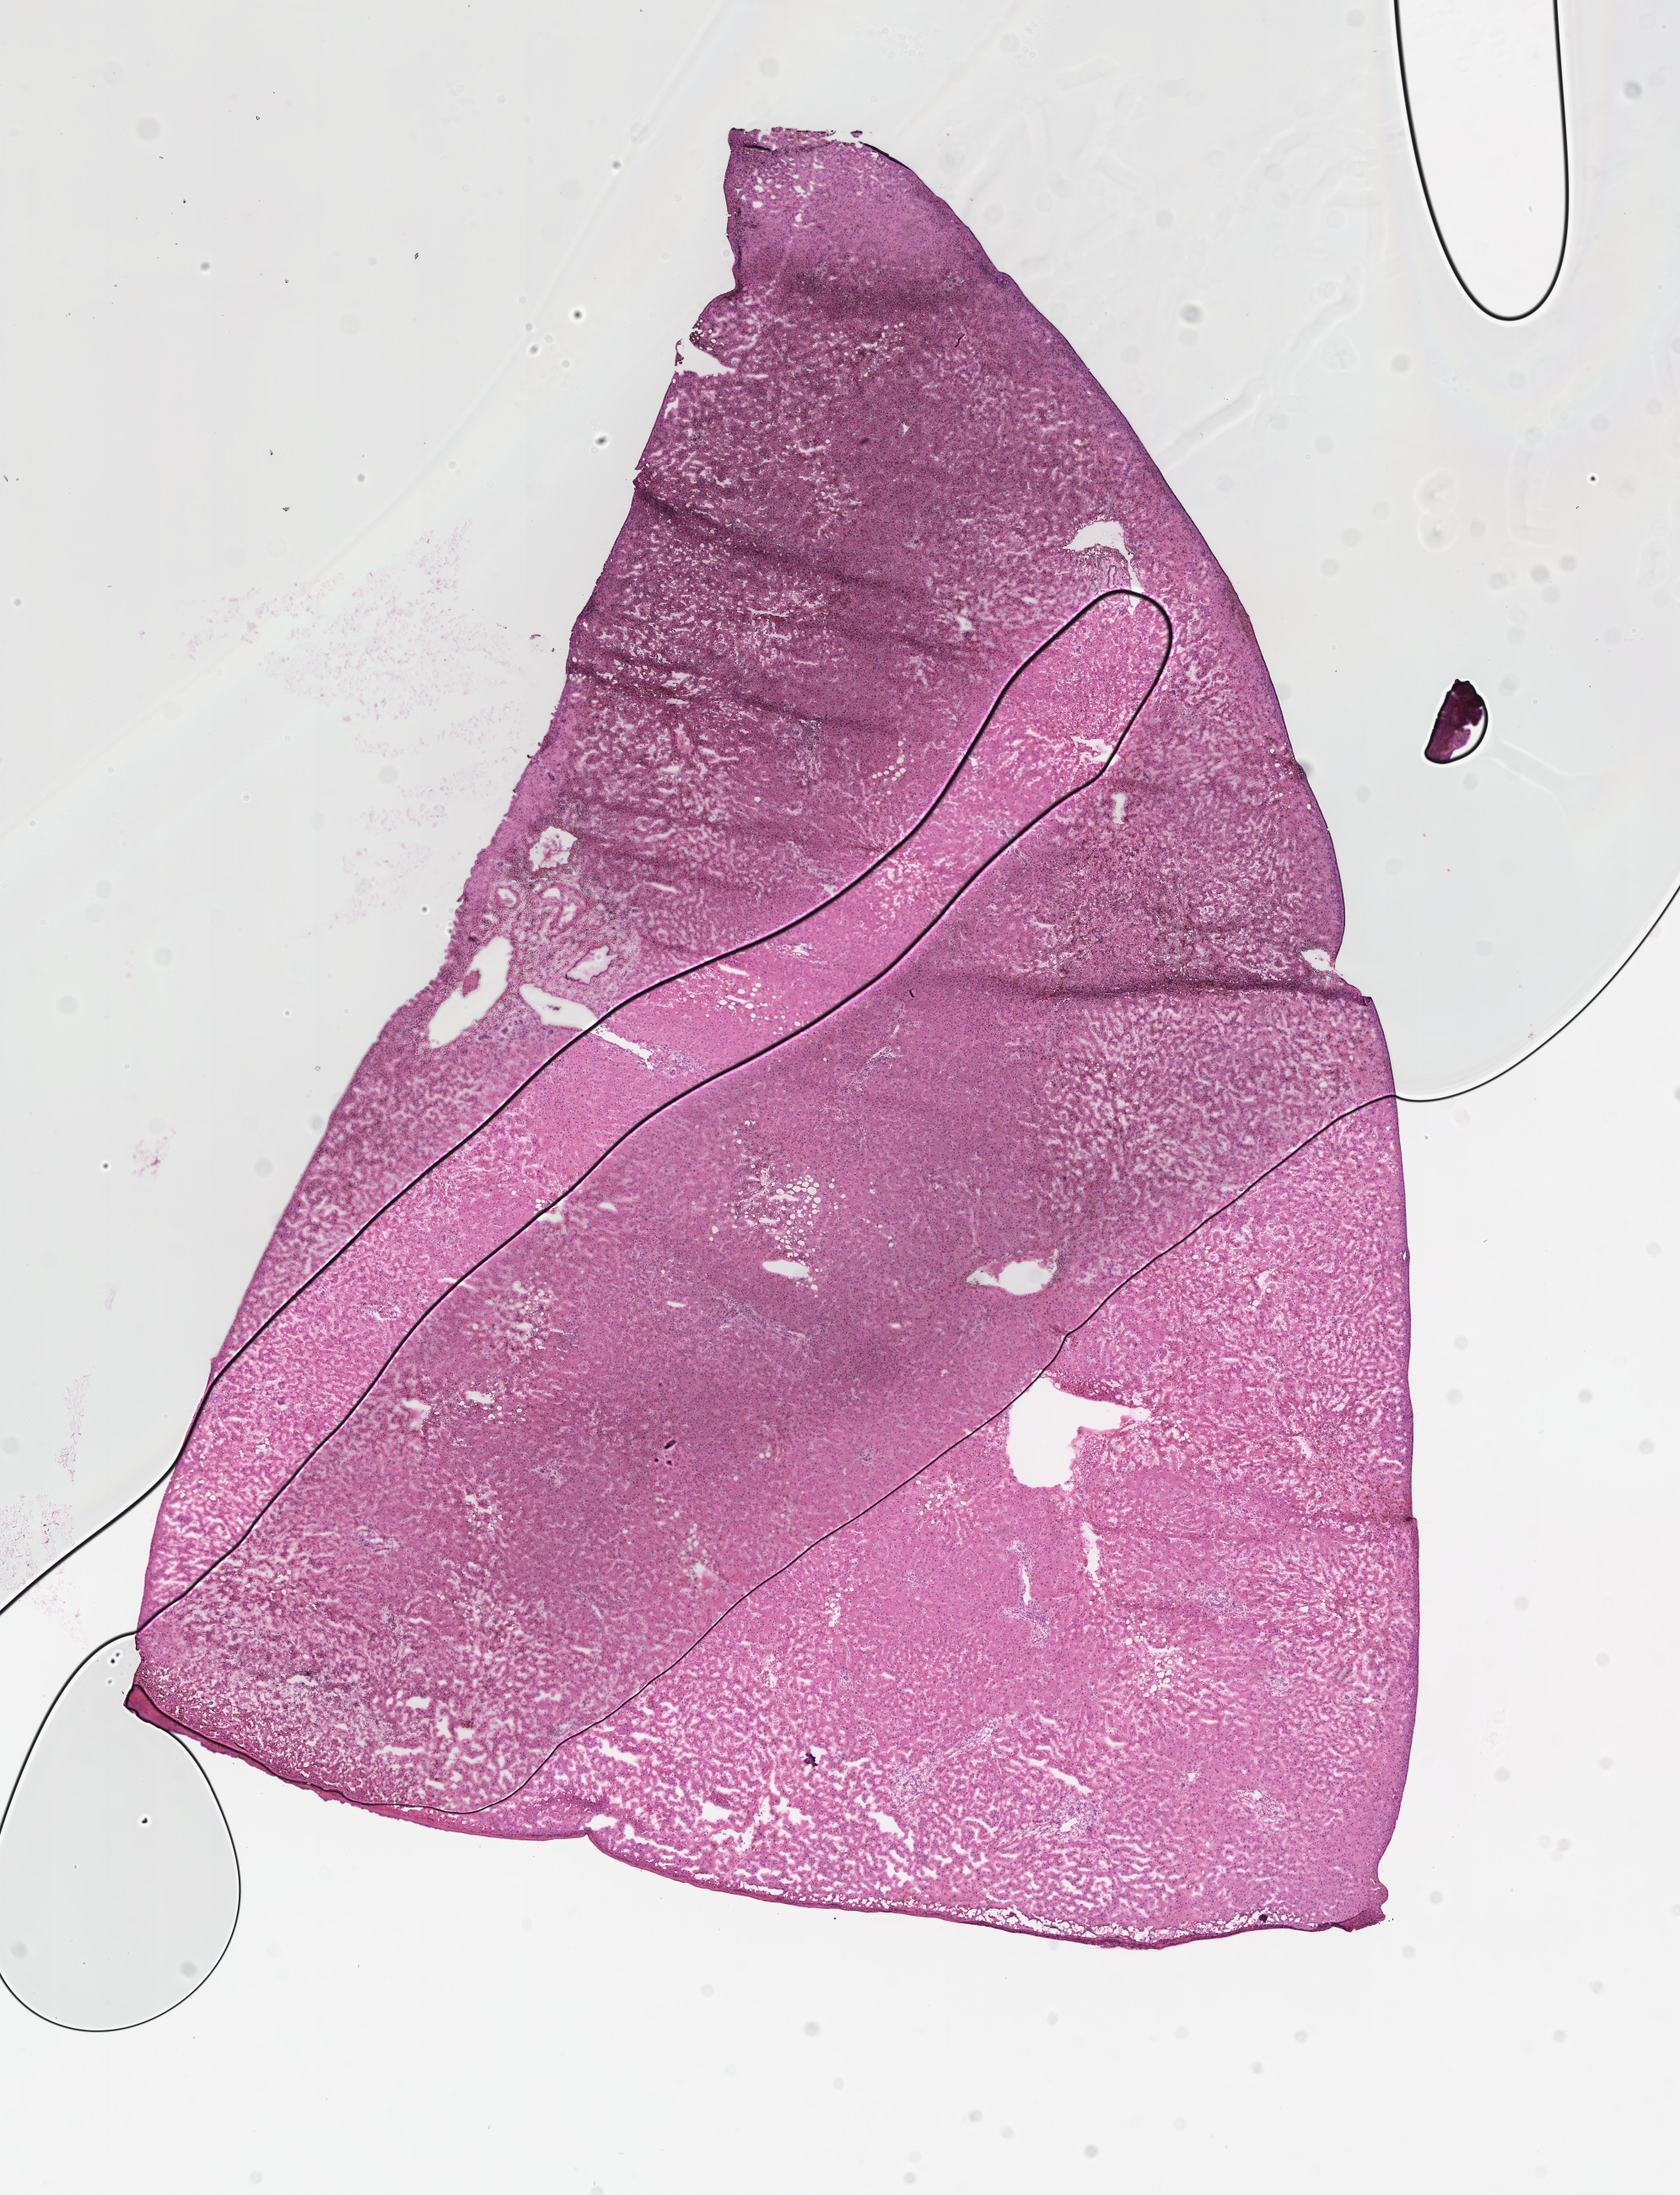
H&E whole-slide image, a low-resolution overview of the entire scanned area, about 8.1 x 10.5 mm. Frozen section (tissue freezing medium). Specimen: non-tumor (normal tissue) sample from a patient with adenocarcinoma, NOS. Site: colon. Male, age 61 years at initial diagnosis. Composition of this section per pathologist review: tumor cells 0%, tumor nuclei 0%, stromal cells 0%, necrosis 0%, normal cells 100%. Infiltration values recorded for this section: lymphocyte infiltration 0%, monocyte infiltration 0%, neutrophil infiltration 0%.
• this section: non-tumor tissue sample; the patient's diagnosis is given above
• section: top of the tissue portion